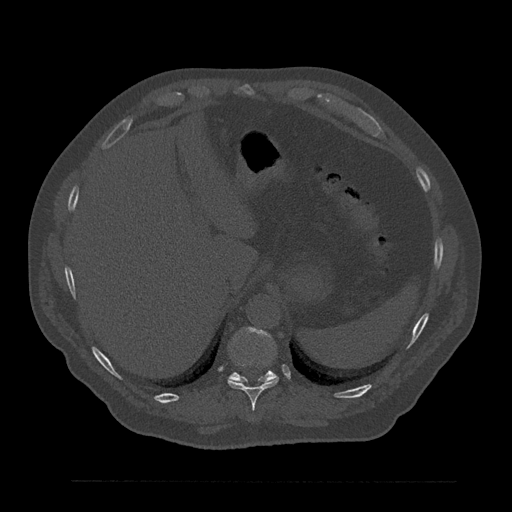
CT including the spine, one axial slice. Slice 329 of 797 in the series (ordered by position). Reconstruction kernel Br40s/3. 120 kVp. Bone window (W 1800 / L 400 HU). 0.5 mm slice thickness. 512 × 512 image matrix, field of view 430 × 430 mm. Patient: male, 61 years. From the clinical record (not read from this slice): primary cancer: prostate.
Outlined on this slice (semi-automatically segmented with operator editing):
- T10 vertebra: box from (x=227, y=363) to (x=278, y=410) px
- T11 vertebra: (x=229, y=328)–(x=276, y=382)